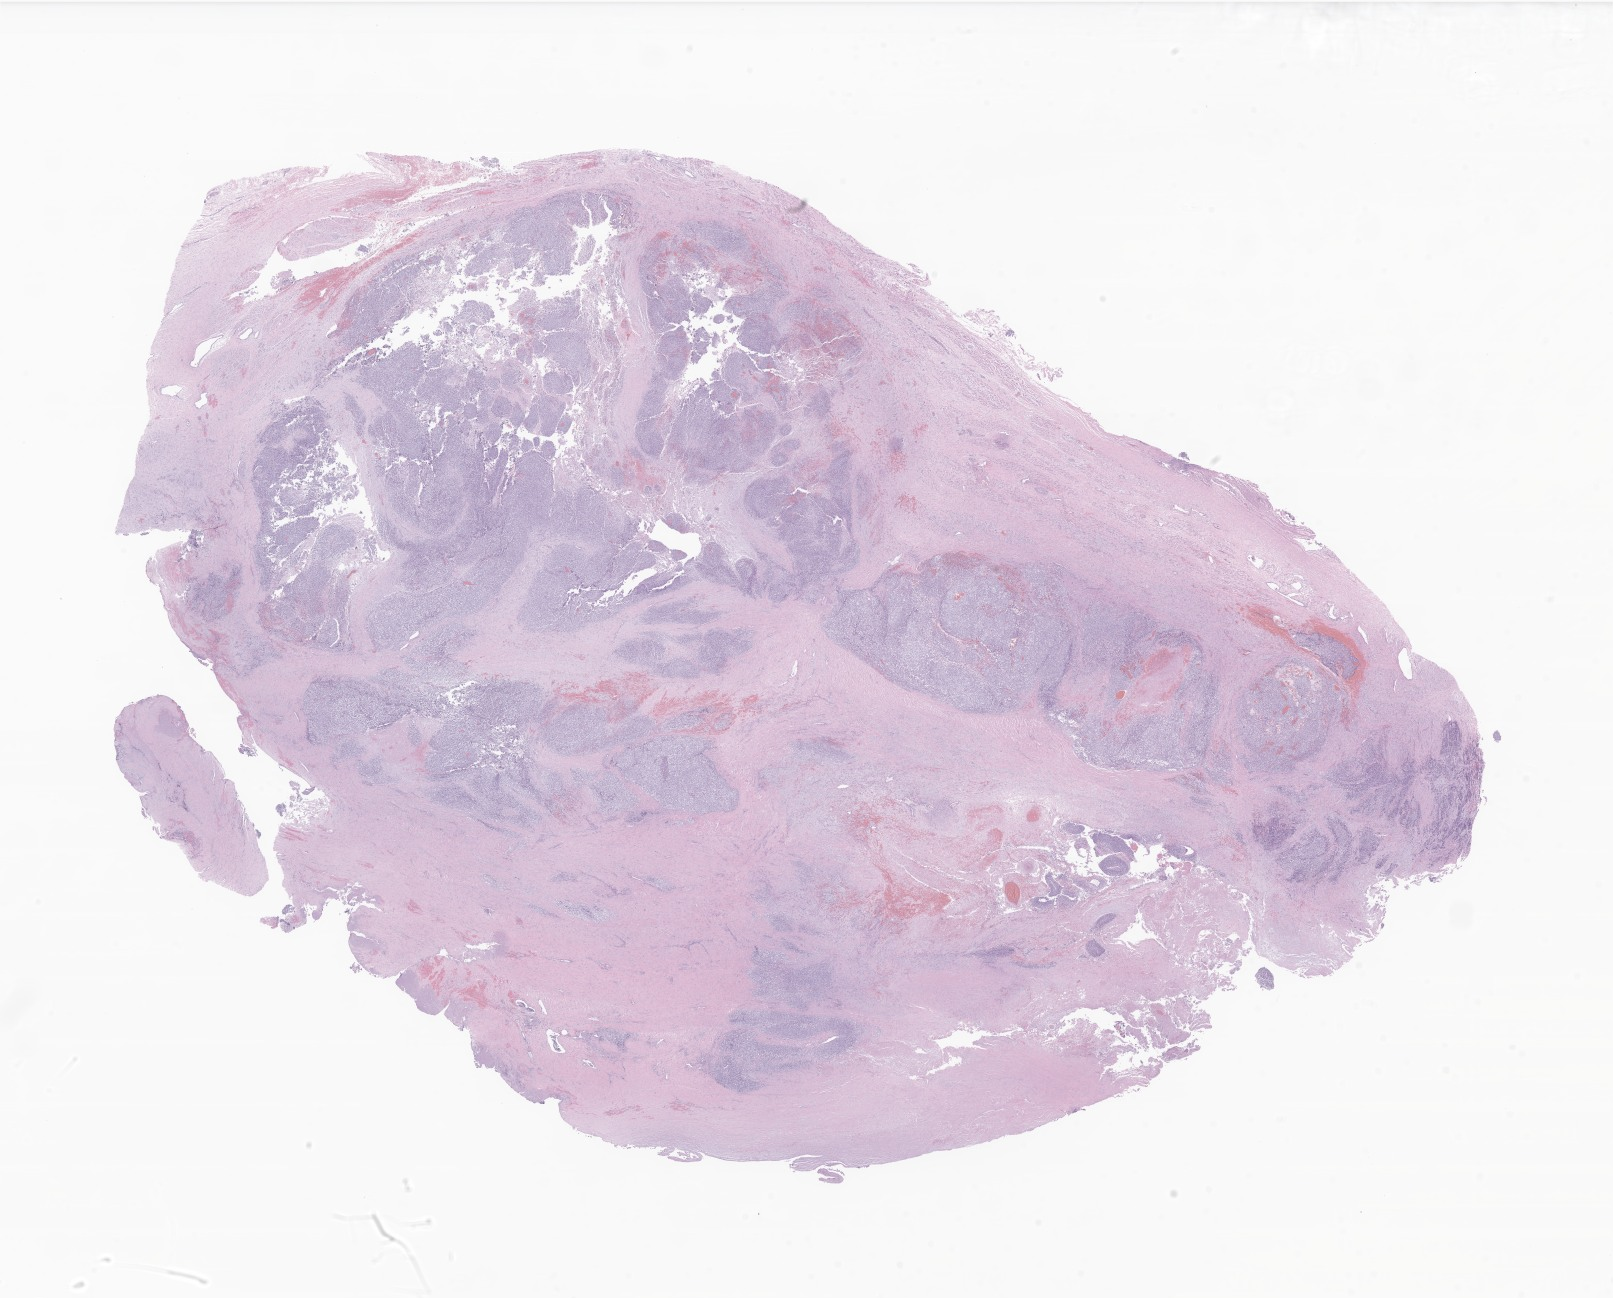
Digitized H&E-stained section of tumor tissue from the head and neck, a low-resolution overview of the entire scanned area, about 27.2 x 21.9 mm. Formalin-fixed, paraffin-embedded (FFPE) tissue. Patient male; age 176 months.
Diagnosis: Small cell sarcoma. Tissue or organ of origin (case record): head, face or neck.